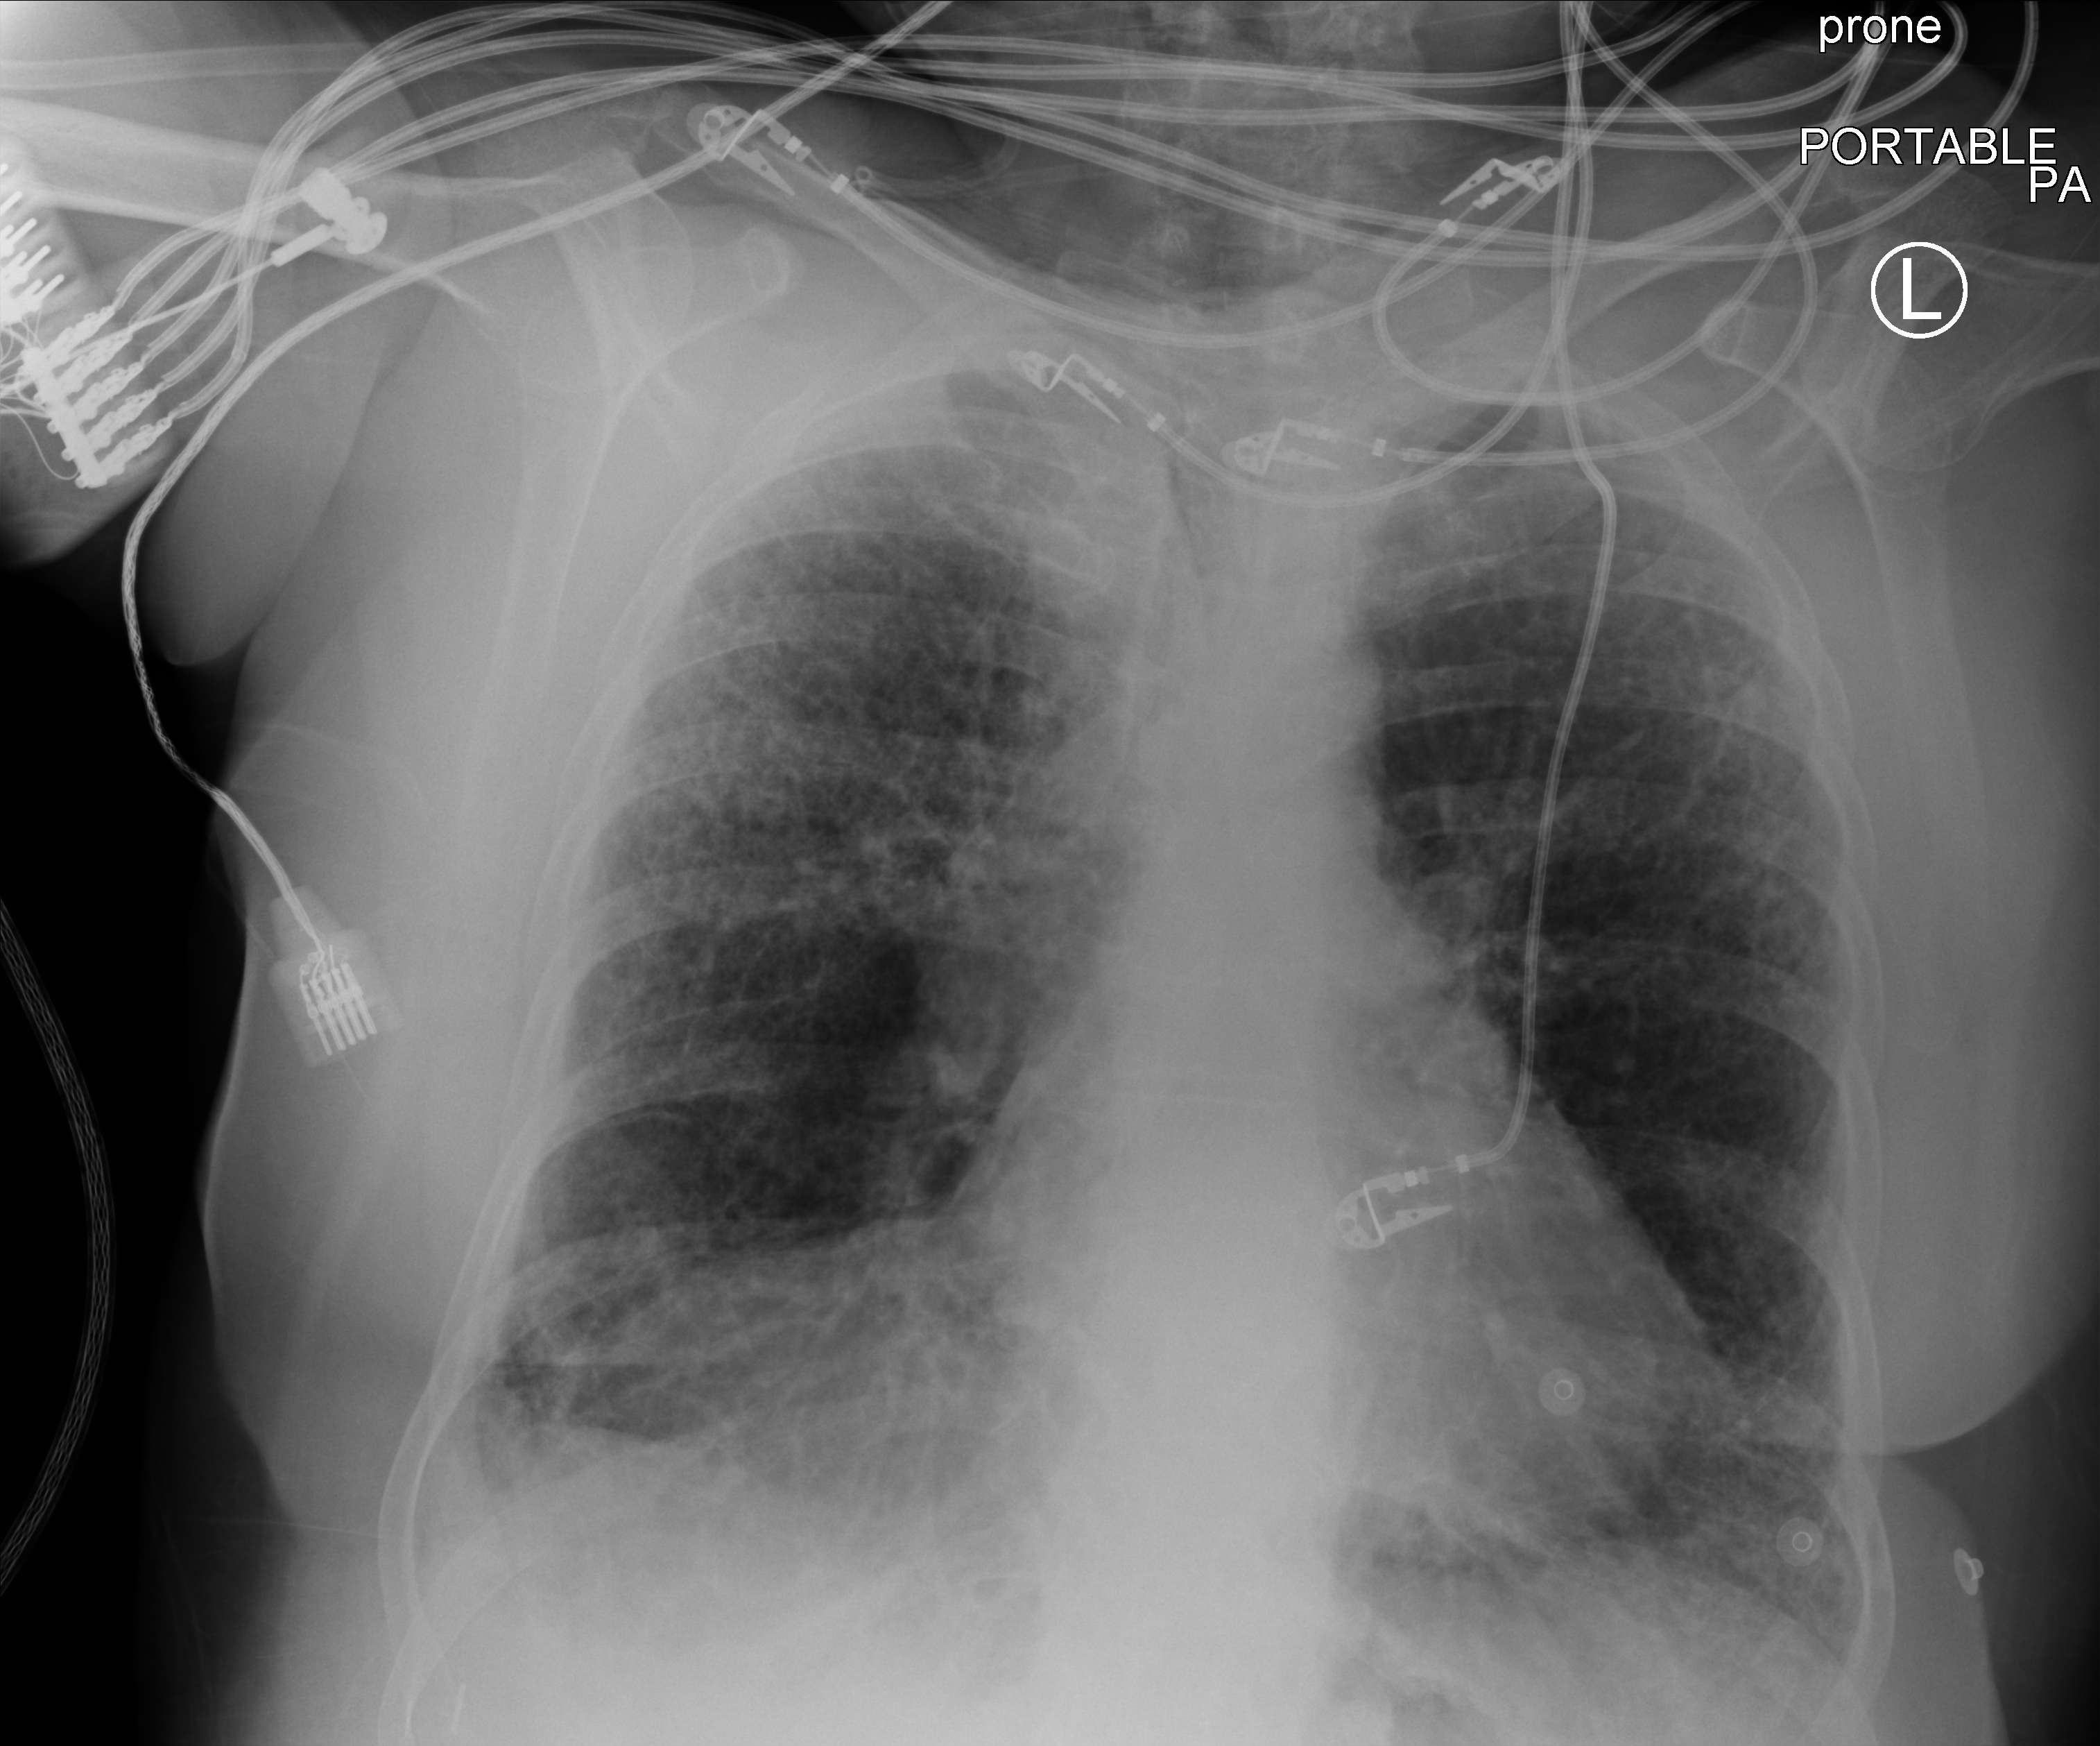
Portable chest radiograph, posteroanterior (PA) projection. Patient hospitalised with COVID-19; female, aged 60–74 years.
From the hospital-stay record, not from the radiograph (when in the stay this image was taken is not recorded): length of hospital stay: 19 days; mechanically ventilated during this hospital stay: yes.